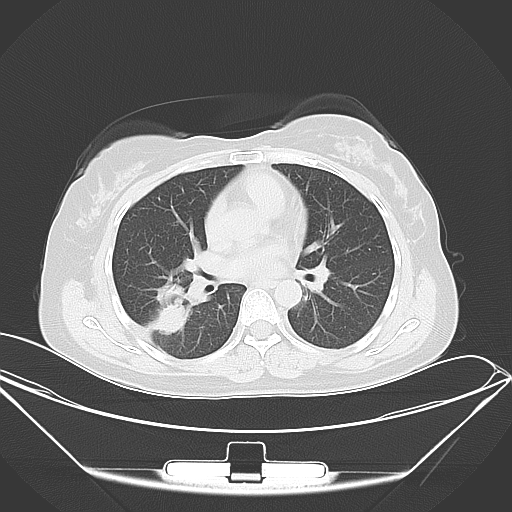
Chest CT, one axial slice; slice 21 of 46 in the series (ordered by position); 120 kVp; lung window (W 1500 / L -600 HU); 512 × 512 image matrix. Female patient, age 42 years. Case-level facts recorded for this patient, not image findings: clinical TNM (as recorded): T1c N0 M1a.
Structures marked on this image (rectangle marked by the reading radiologist):
- lung tumour (recorded histology: adenocarcinoma): bounding box (x1, y1, x2, y2) in pixels: (144, 284, 195, 343)